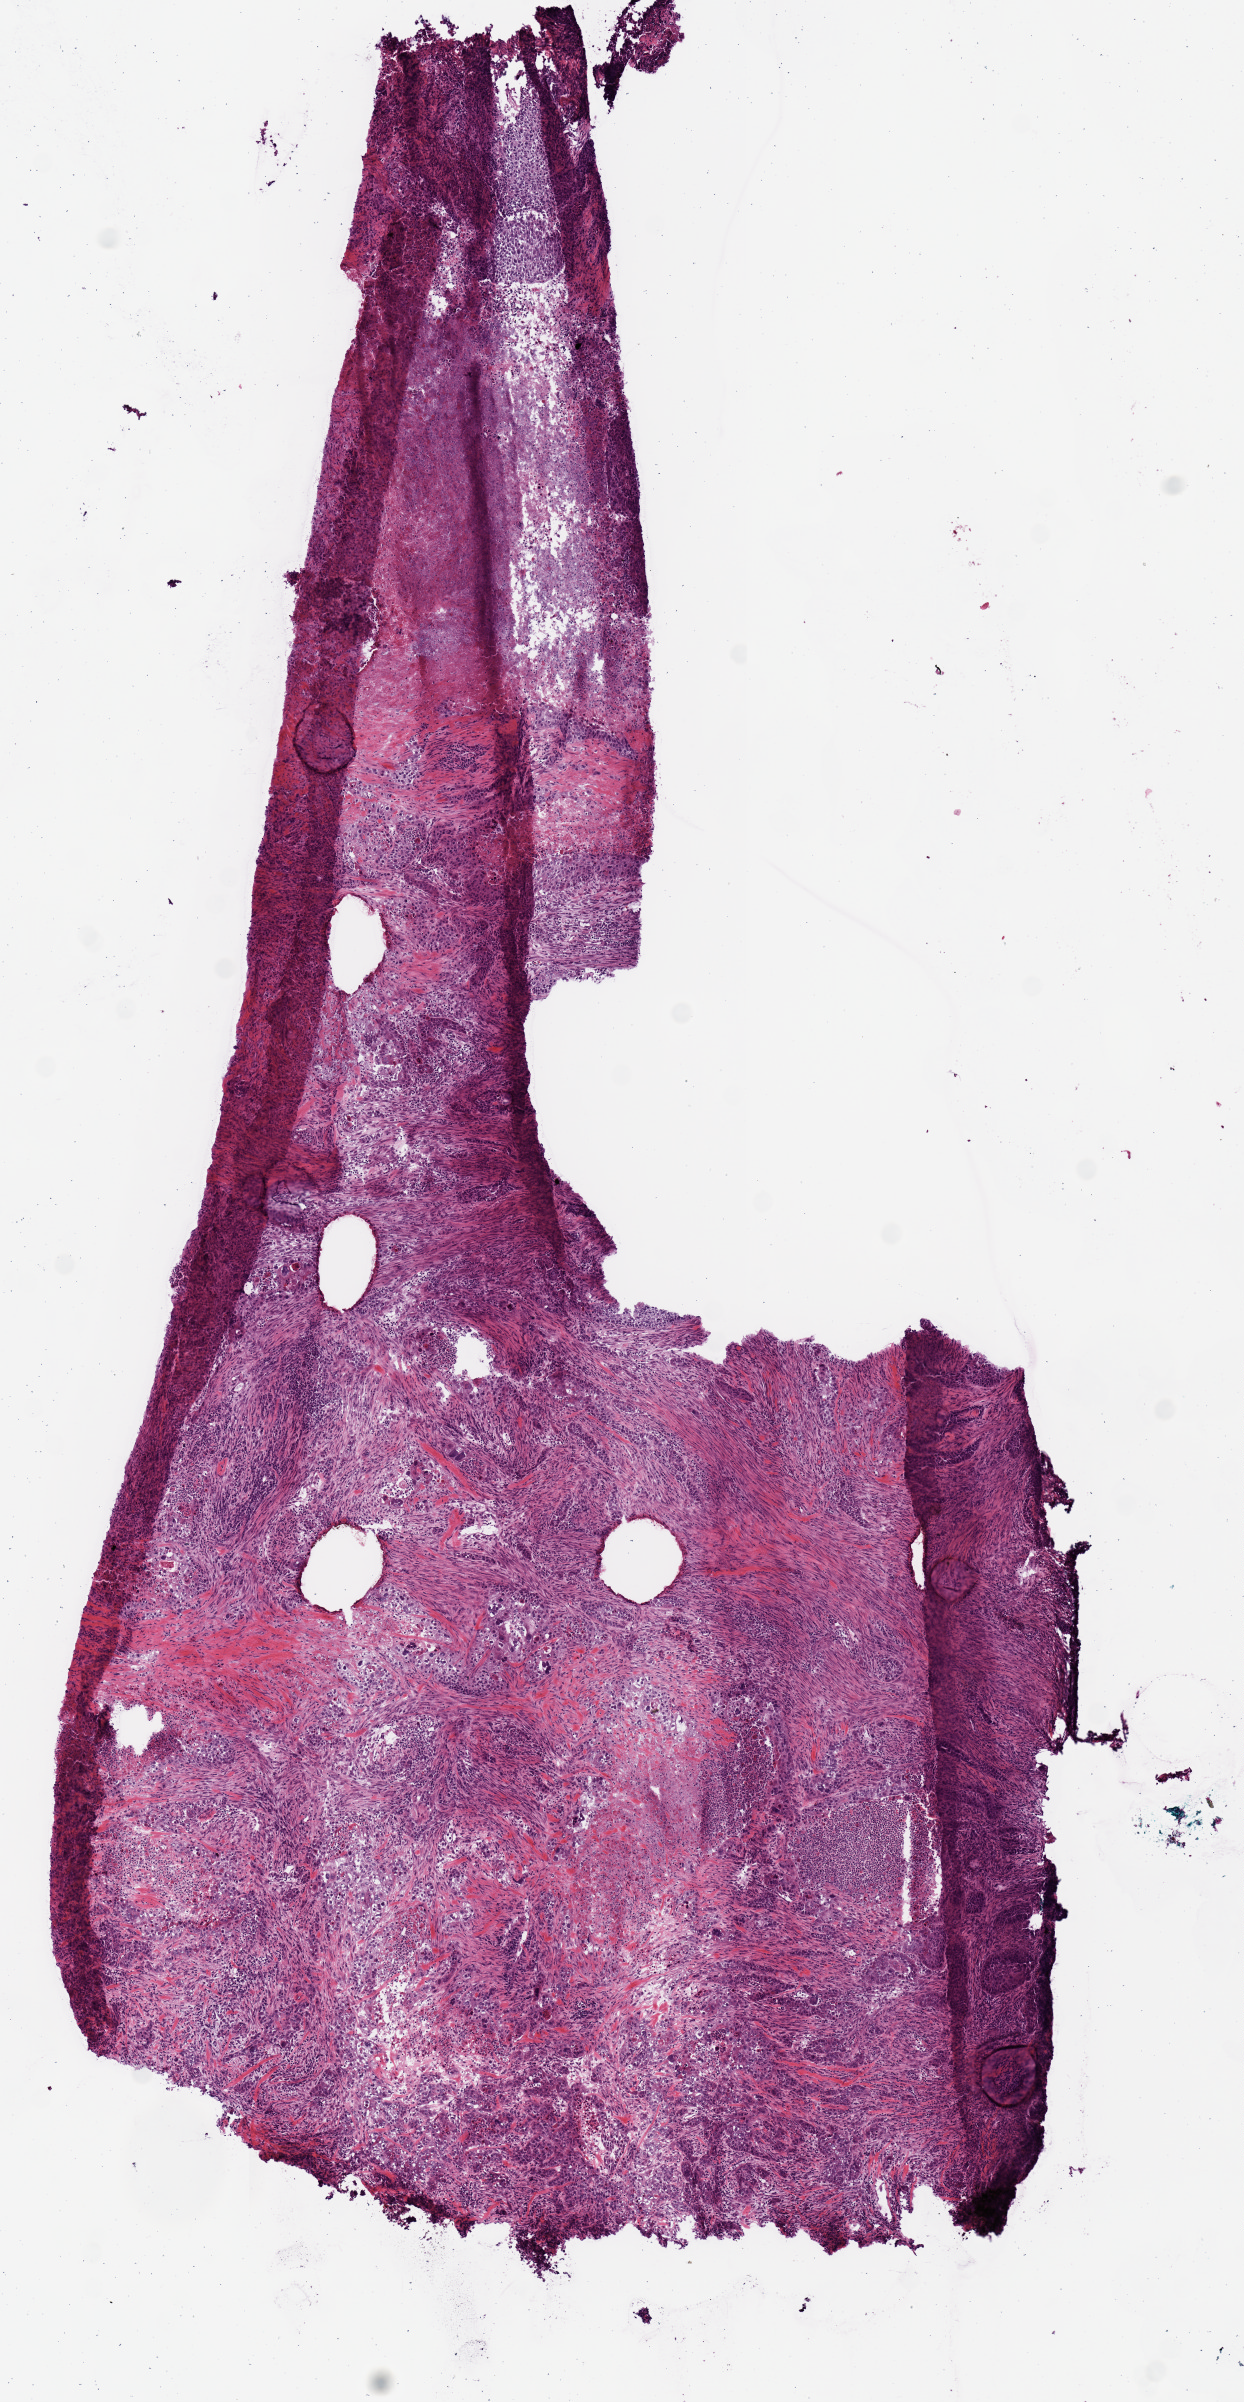
Digitized Hematoxylin and eosin (H&E) stained tissue section (whole slide), shown as a low-resolution overview of the whole scanned area (about 4.9 x 9.5 mm, from a 20x scan). Frozen section from the top of the tissue portion. Sample: primary tumour, lung. Female patient; age at initial diagnosis 74 years. Pathologist review of this section (percent, as recorded): tumour nuclei 60%, necrosis 18%.
Diagnosis: Squamous cell carcinoma, NOS (lower lobe, lung). AJCC pathologic stage: IIB.